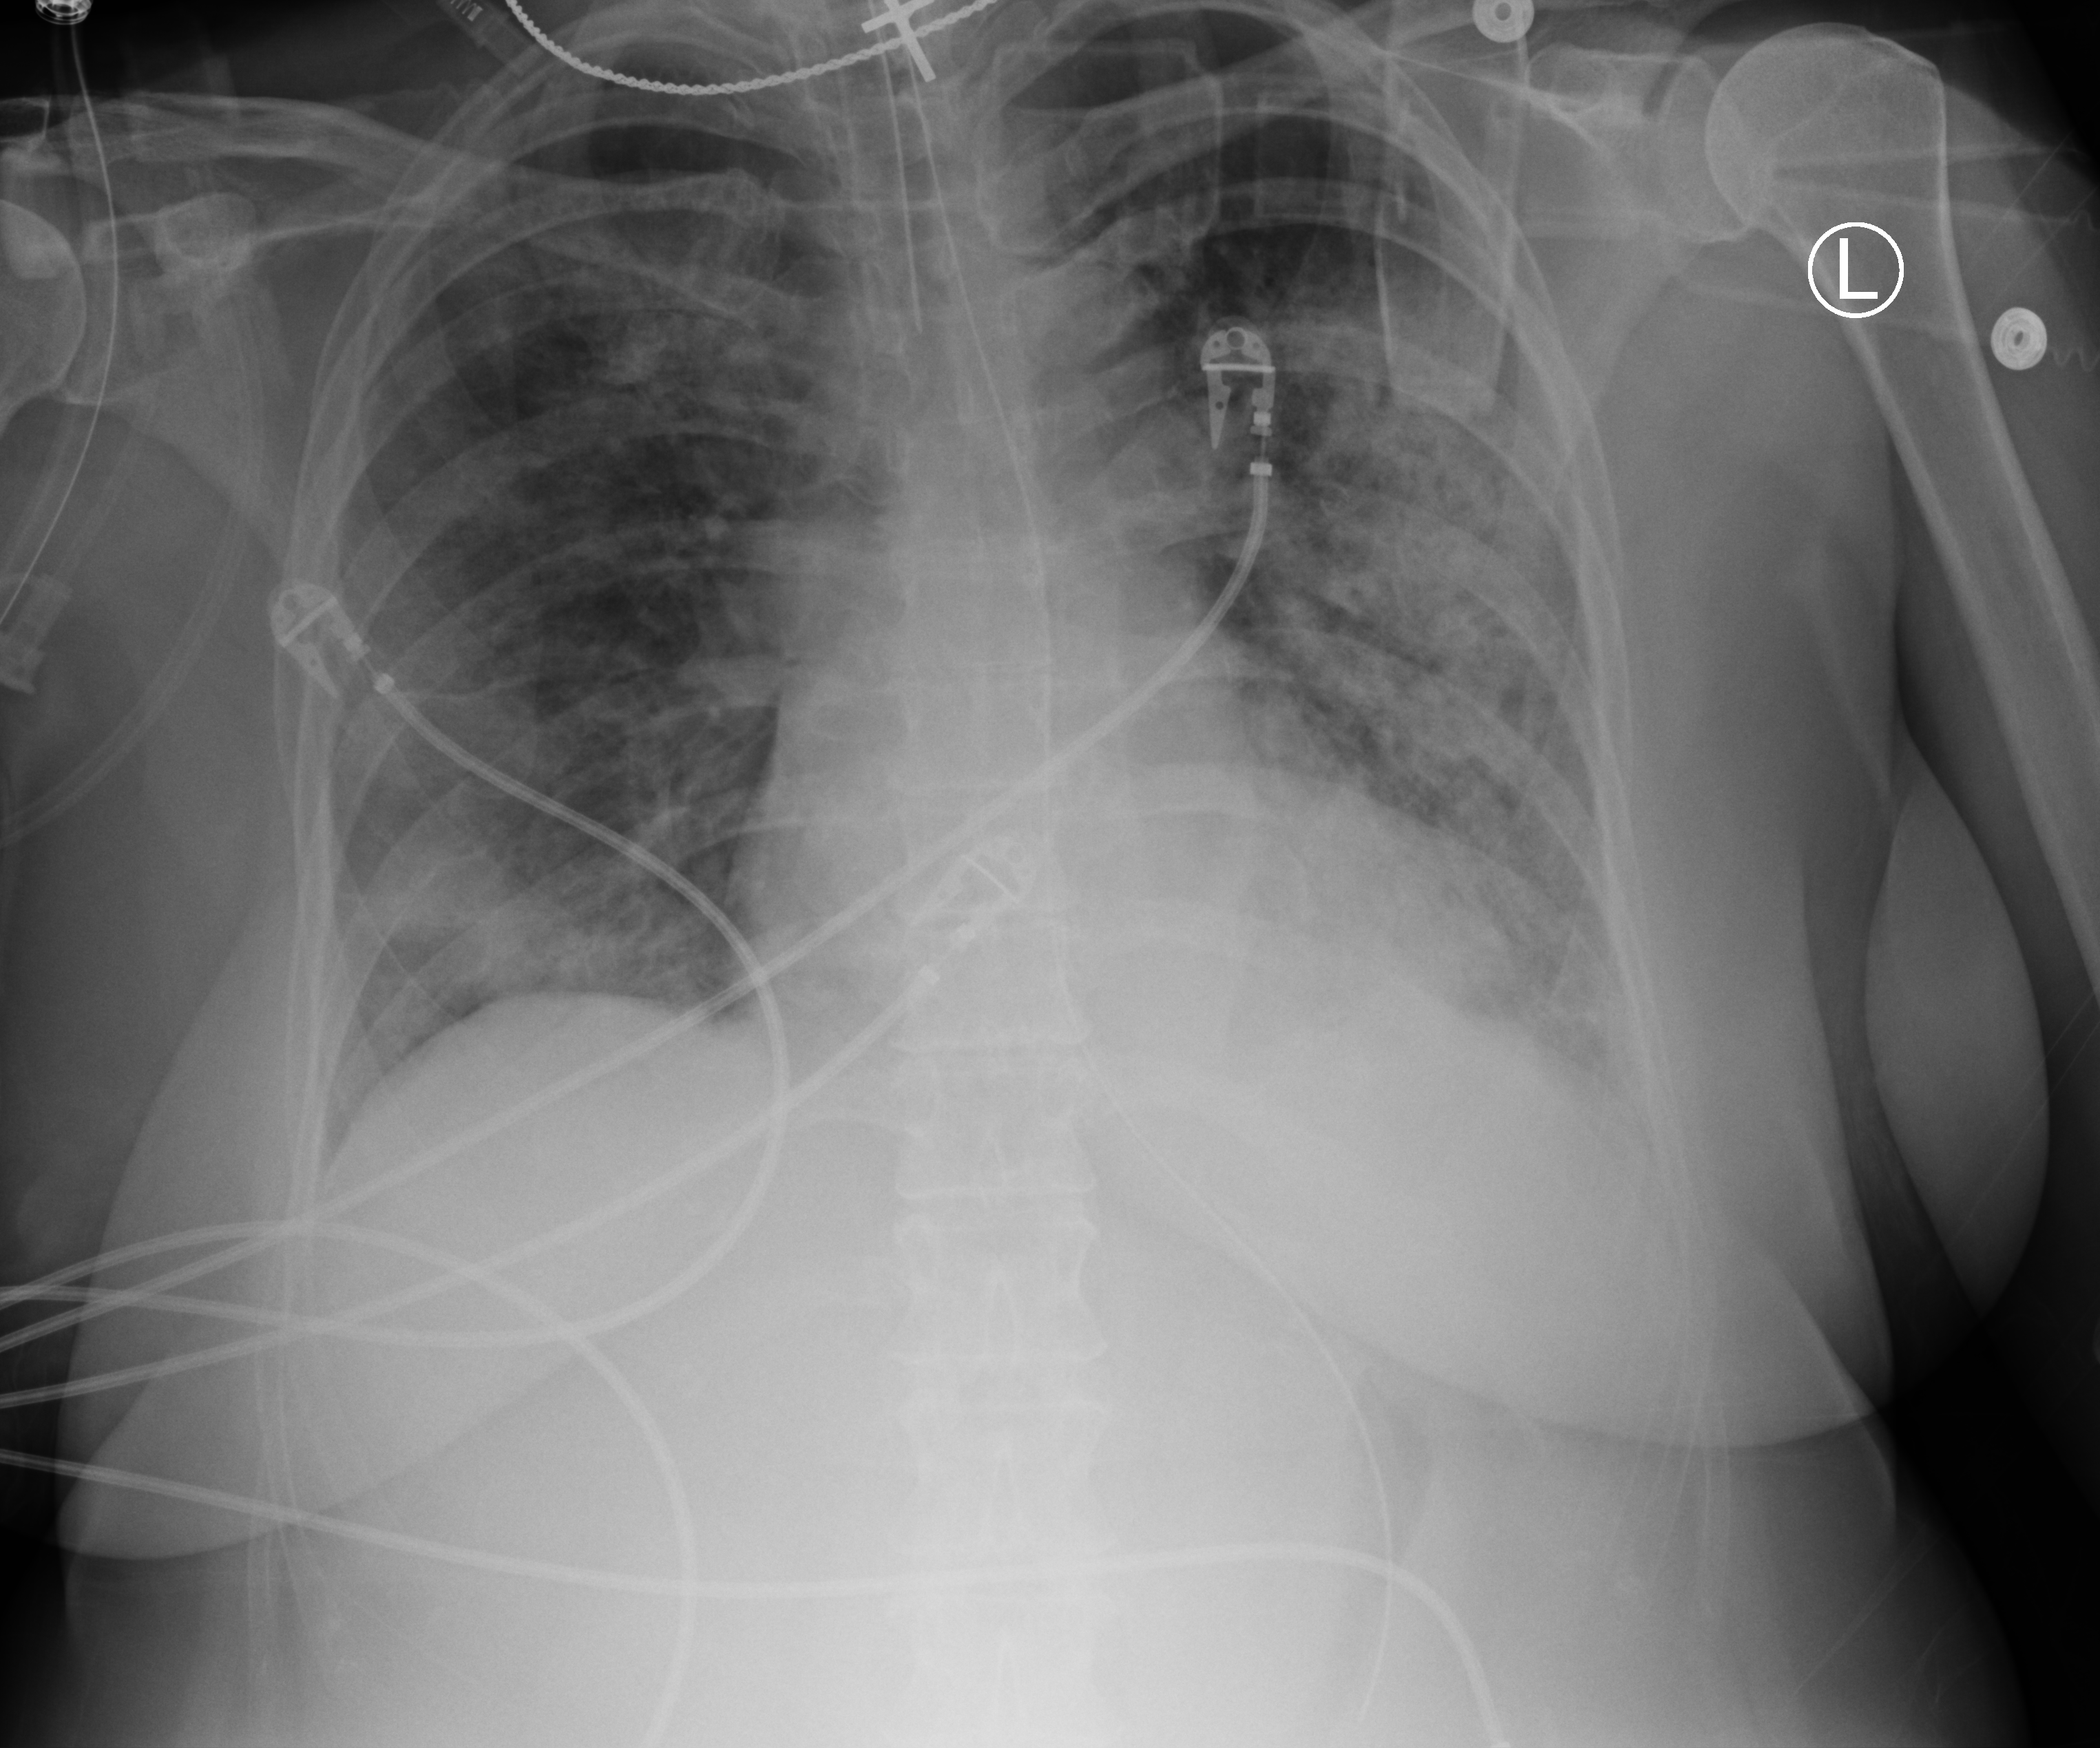
Portable chest radiograph. Female patient hospitalised with COVID-19, age 18–59 years.
Admission-level facts for this patient (not findings on this image; timing relative to this image not recorded): admitted to intensive care during this hospital stay: yes; mechanically ventilated during this hospital stay: yes.